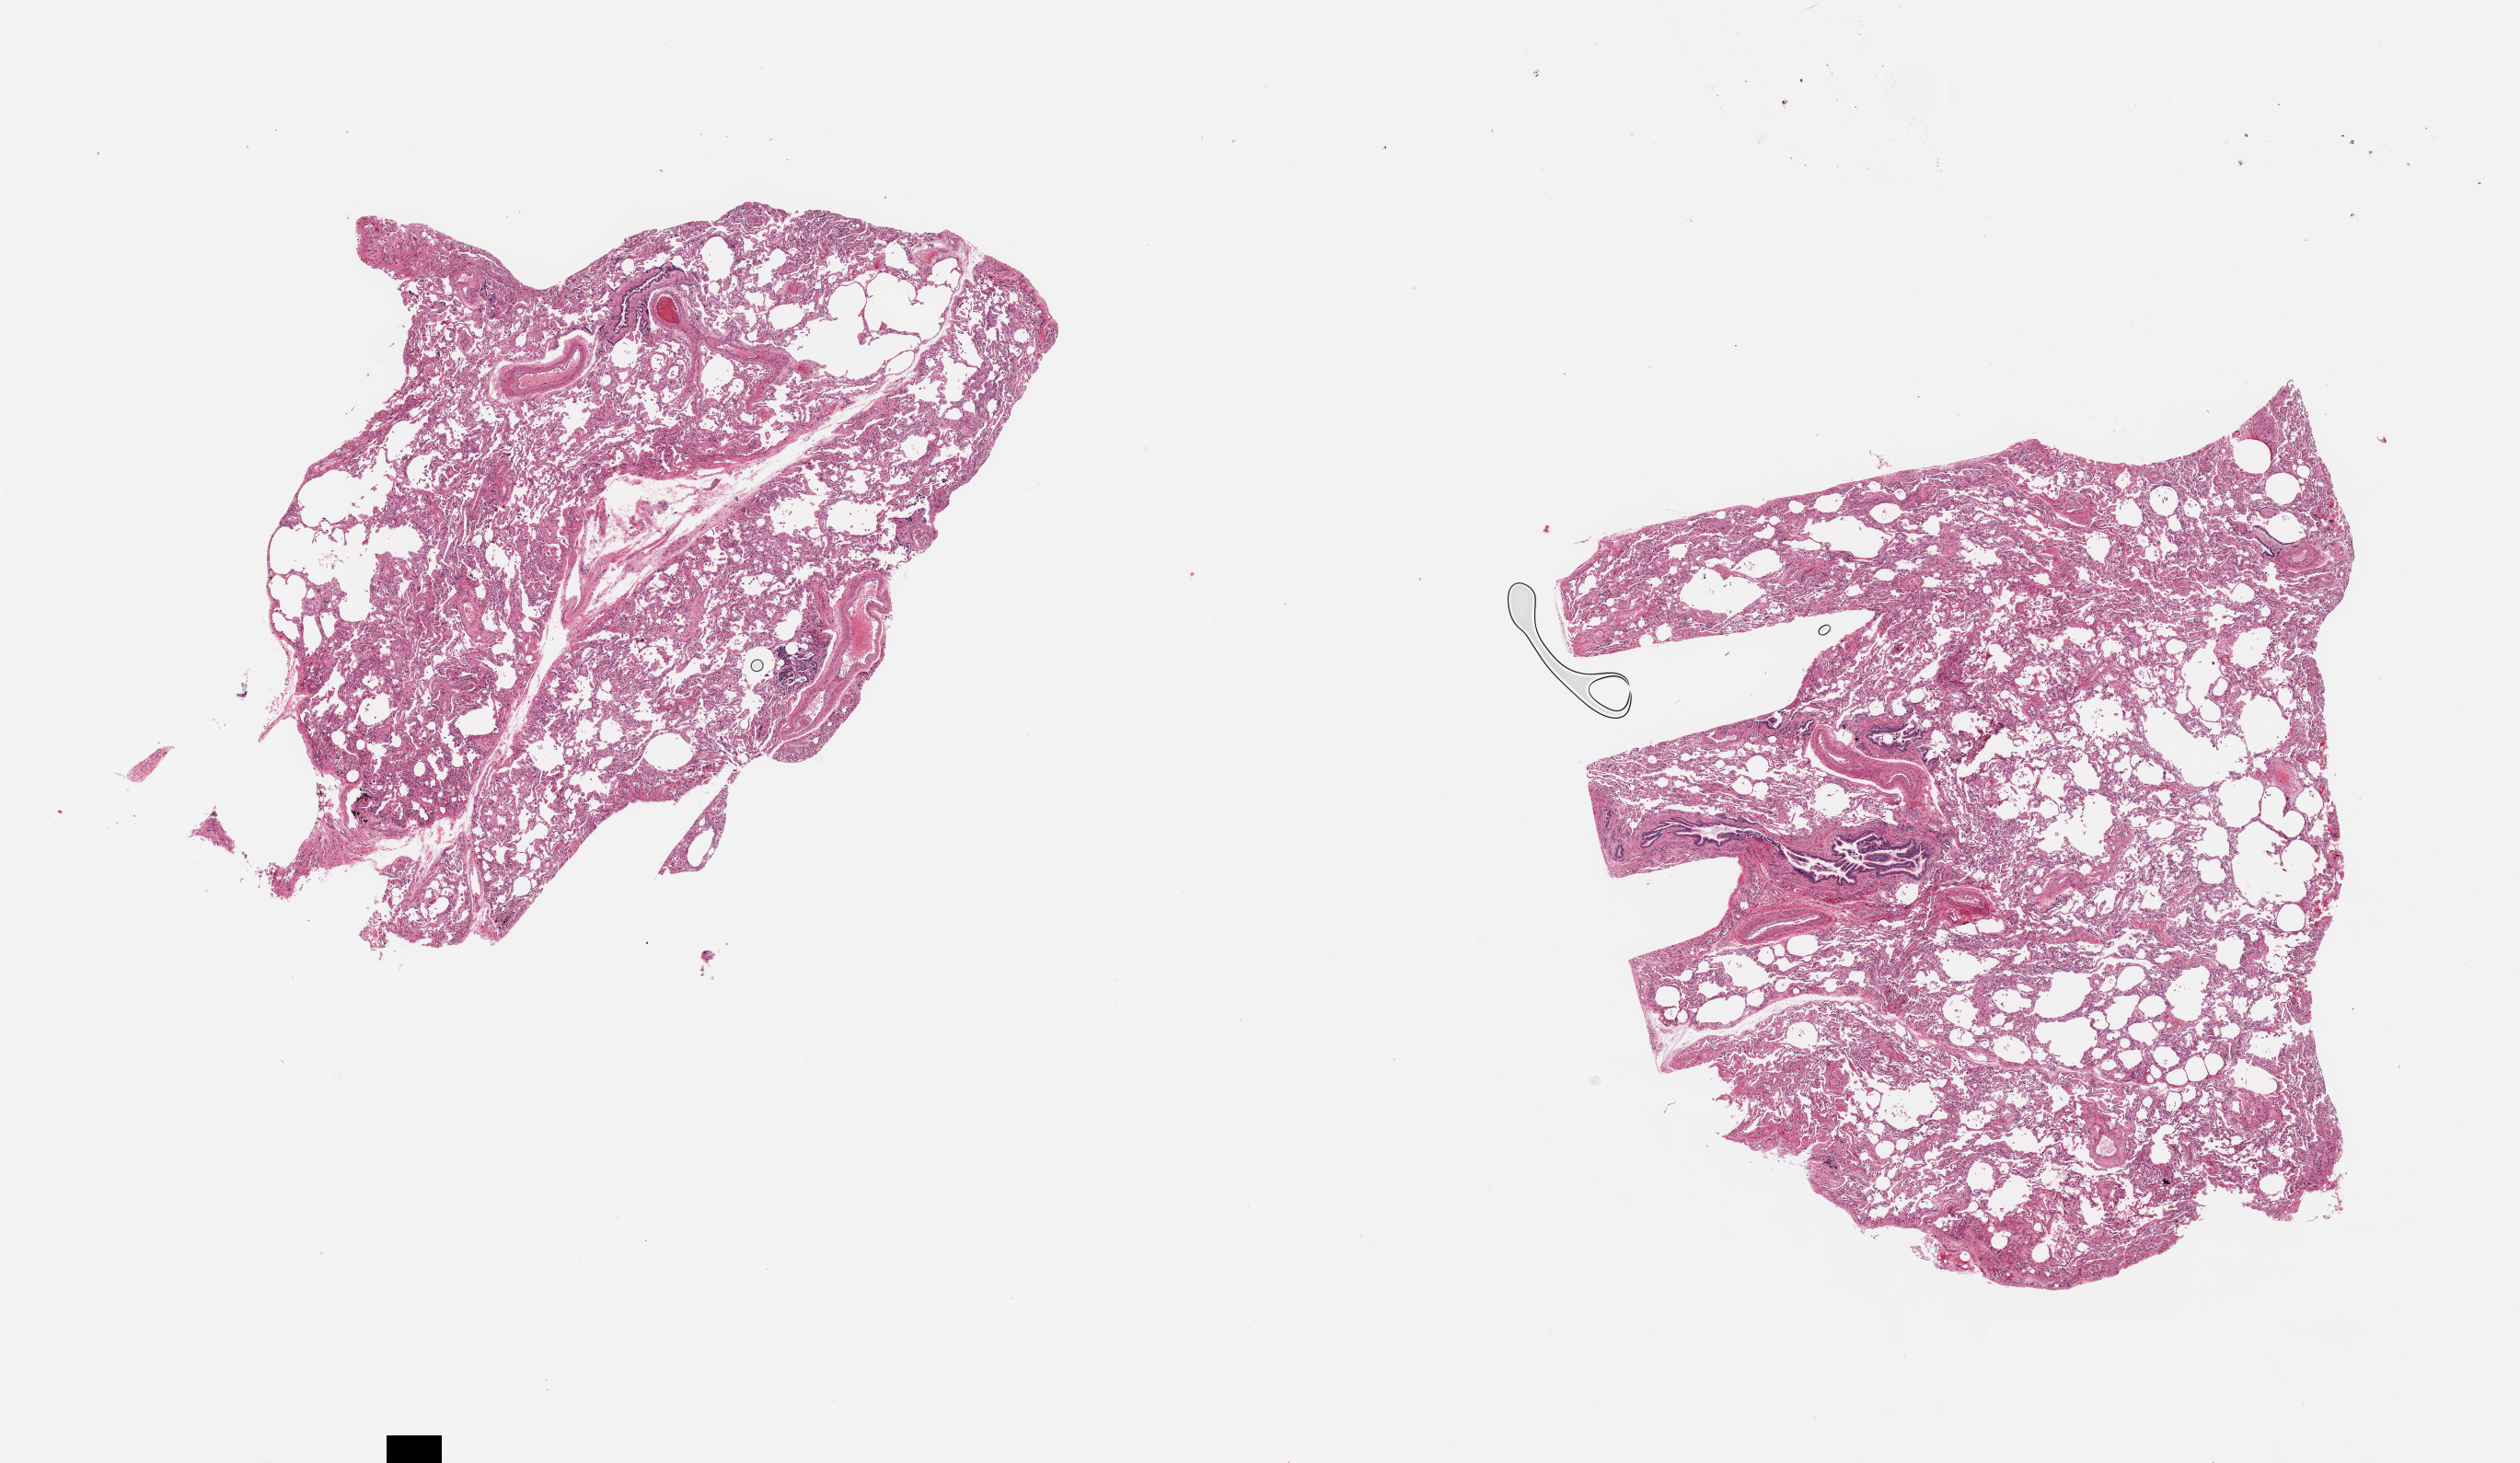
Whole-slide image, hematoxylin and eosin (H&E) stain, whole scanned area (about 21.7 x 12.6 mm, from a 20x scan) shown as a low-resolution overview. PAXgene-fixed paraffin-embedded (PFPE) section. Sampled site (target tissue): lung. Tissue donor sample. Donor sex: male.
Review note (as recorded): 2 pieces, mild congestion; well preserved bronchial mucosa; Foci of bronchial metaplasia noted.